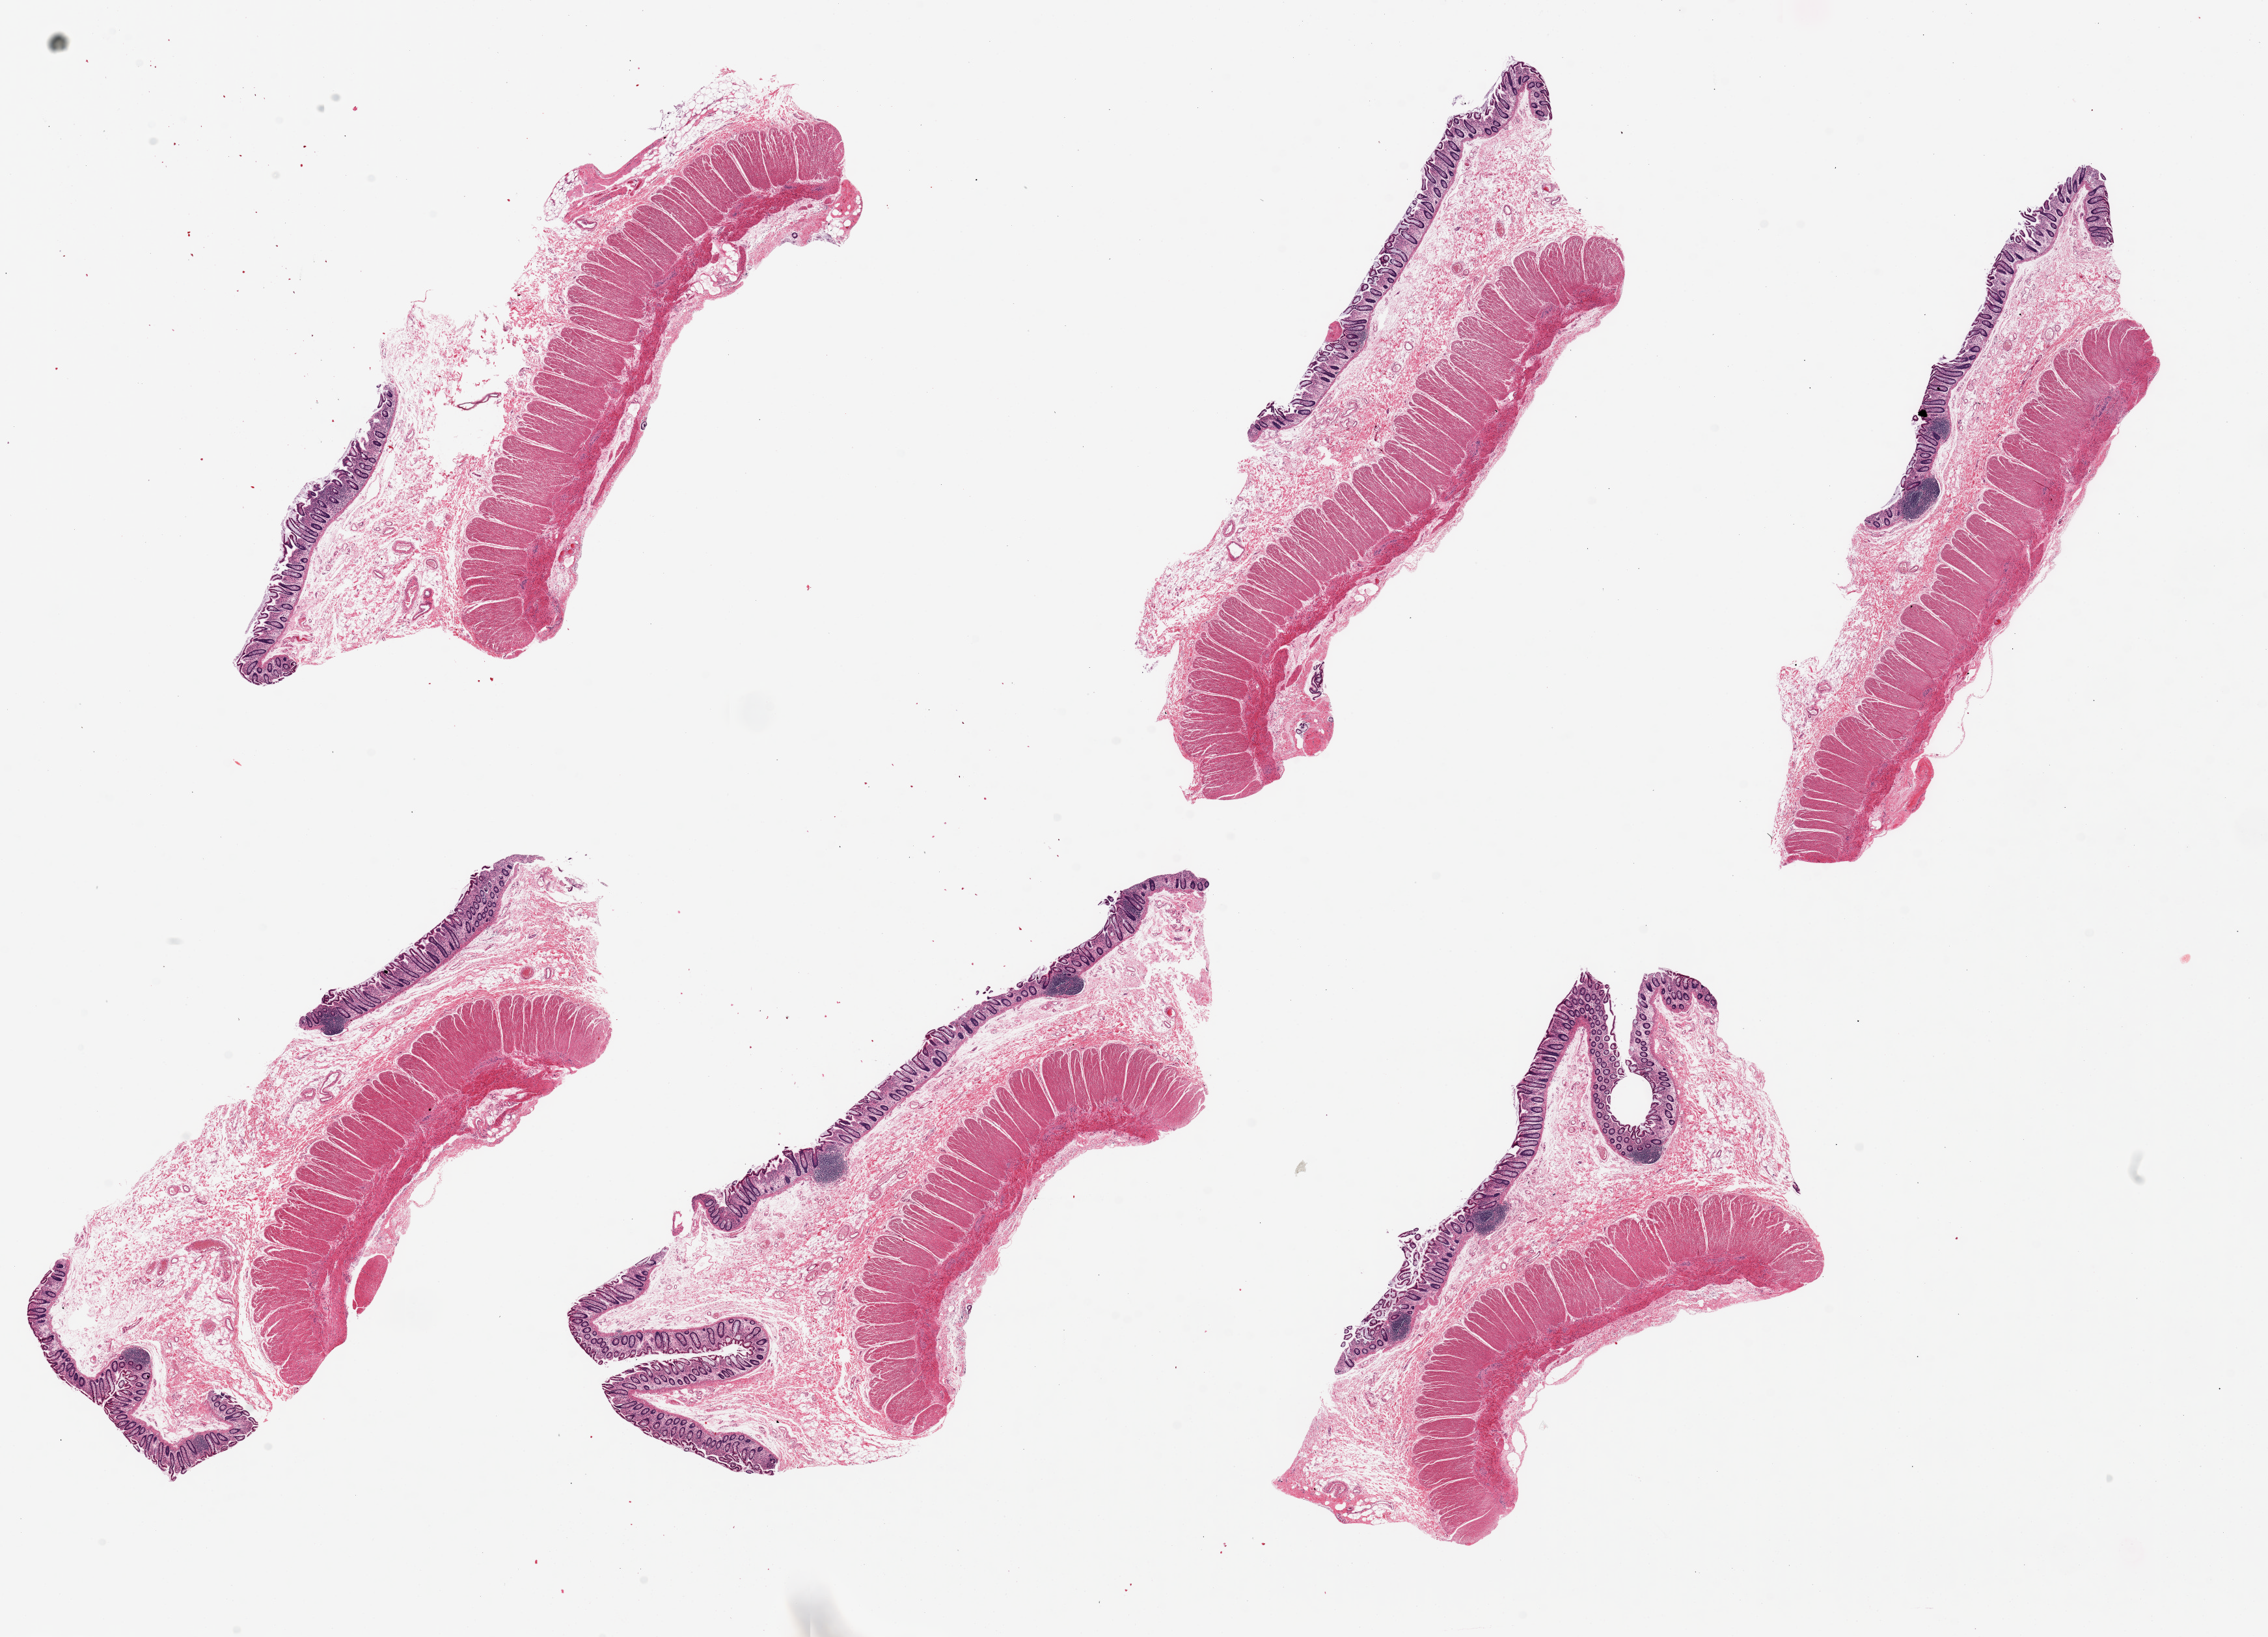
Whole-slide image, haematoxylin and eosin stain, brightfield, a low-resolution overview of the entire scanned area, about 27.6 x 19.9 mm (acquisition: 20x scan), PAXgene-fixed, paraffin-embedded tissue, target tissue: transverse colon, tissue donor sample.
• reviewer comment on this tissue sample: 6 pieces, up to 10x3mm; mucosa moderately autolyzed; muscle slightly autolyzed